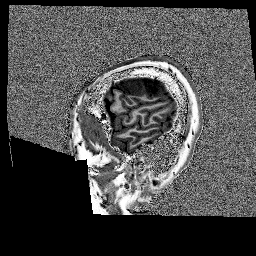
Brain MRI from a brain-tumour surgery series, one sagittal slice. Slice 29 of 176 in the series (ordered by position). 256 × 256 image matrix, field of view 256 × 256 mm. From the clinical record (not read from this slice): histopathology: Glioblastoma; WHO grade: 4; IDH mutation: no.
Annotated regions visible in this slice (outlined manually by an expert reader):
- tumour: bounding box [x1, y1, x2, y2] px = [118, 76, 175, 98]